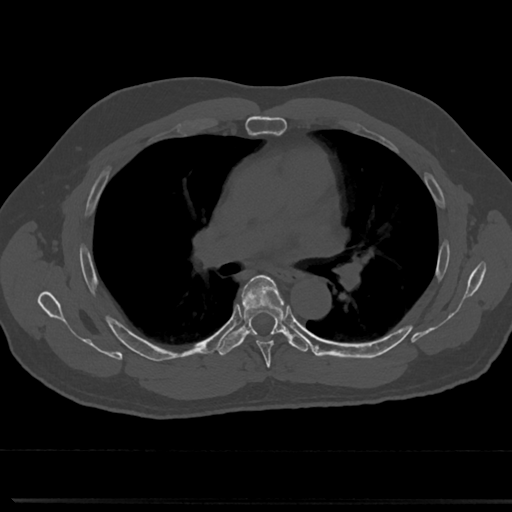
CT including the spine, one axial slice; position 473 of 817 along the scan axis; reconstruction kernel Br40s/3; bone window (W 1800 / L 400 HU); 0.5 mm slice thickness; 512 × 512 image matrix. Male patient, age 61 years. From the clinical record (not read from this slice): primary cancer: prostate.
Structures marked on this image (semi-automatic segmentation, software-assisted and operator-edited):
- T5 vertebra: bounding box <239,277,287,361> (left, top, right, bottom; pixels)
- T6 vertebra: <221,276,287,352>